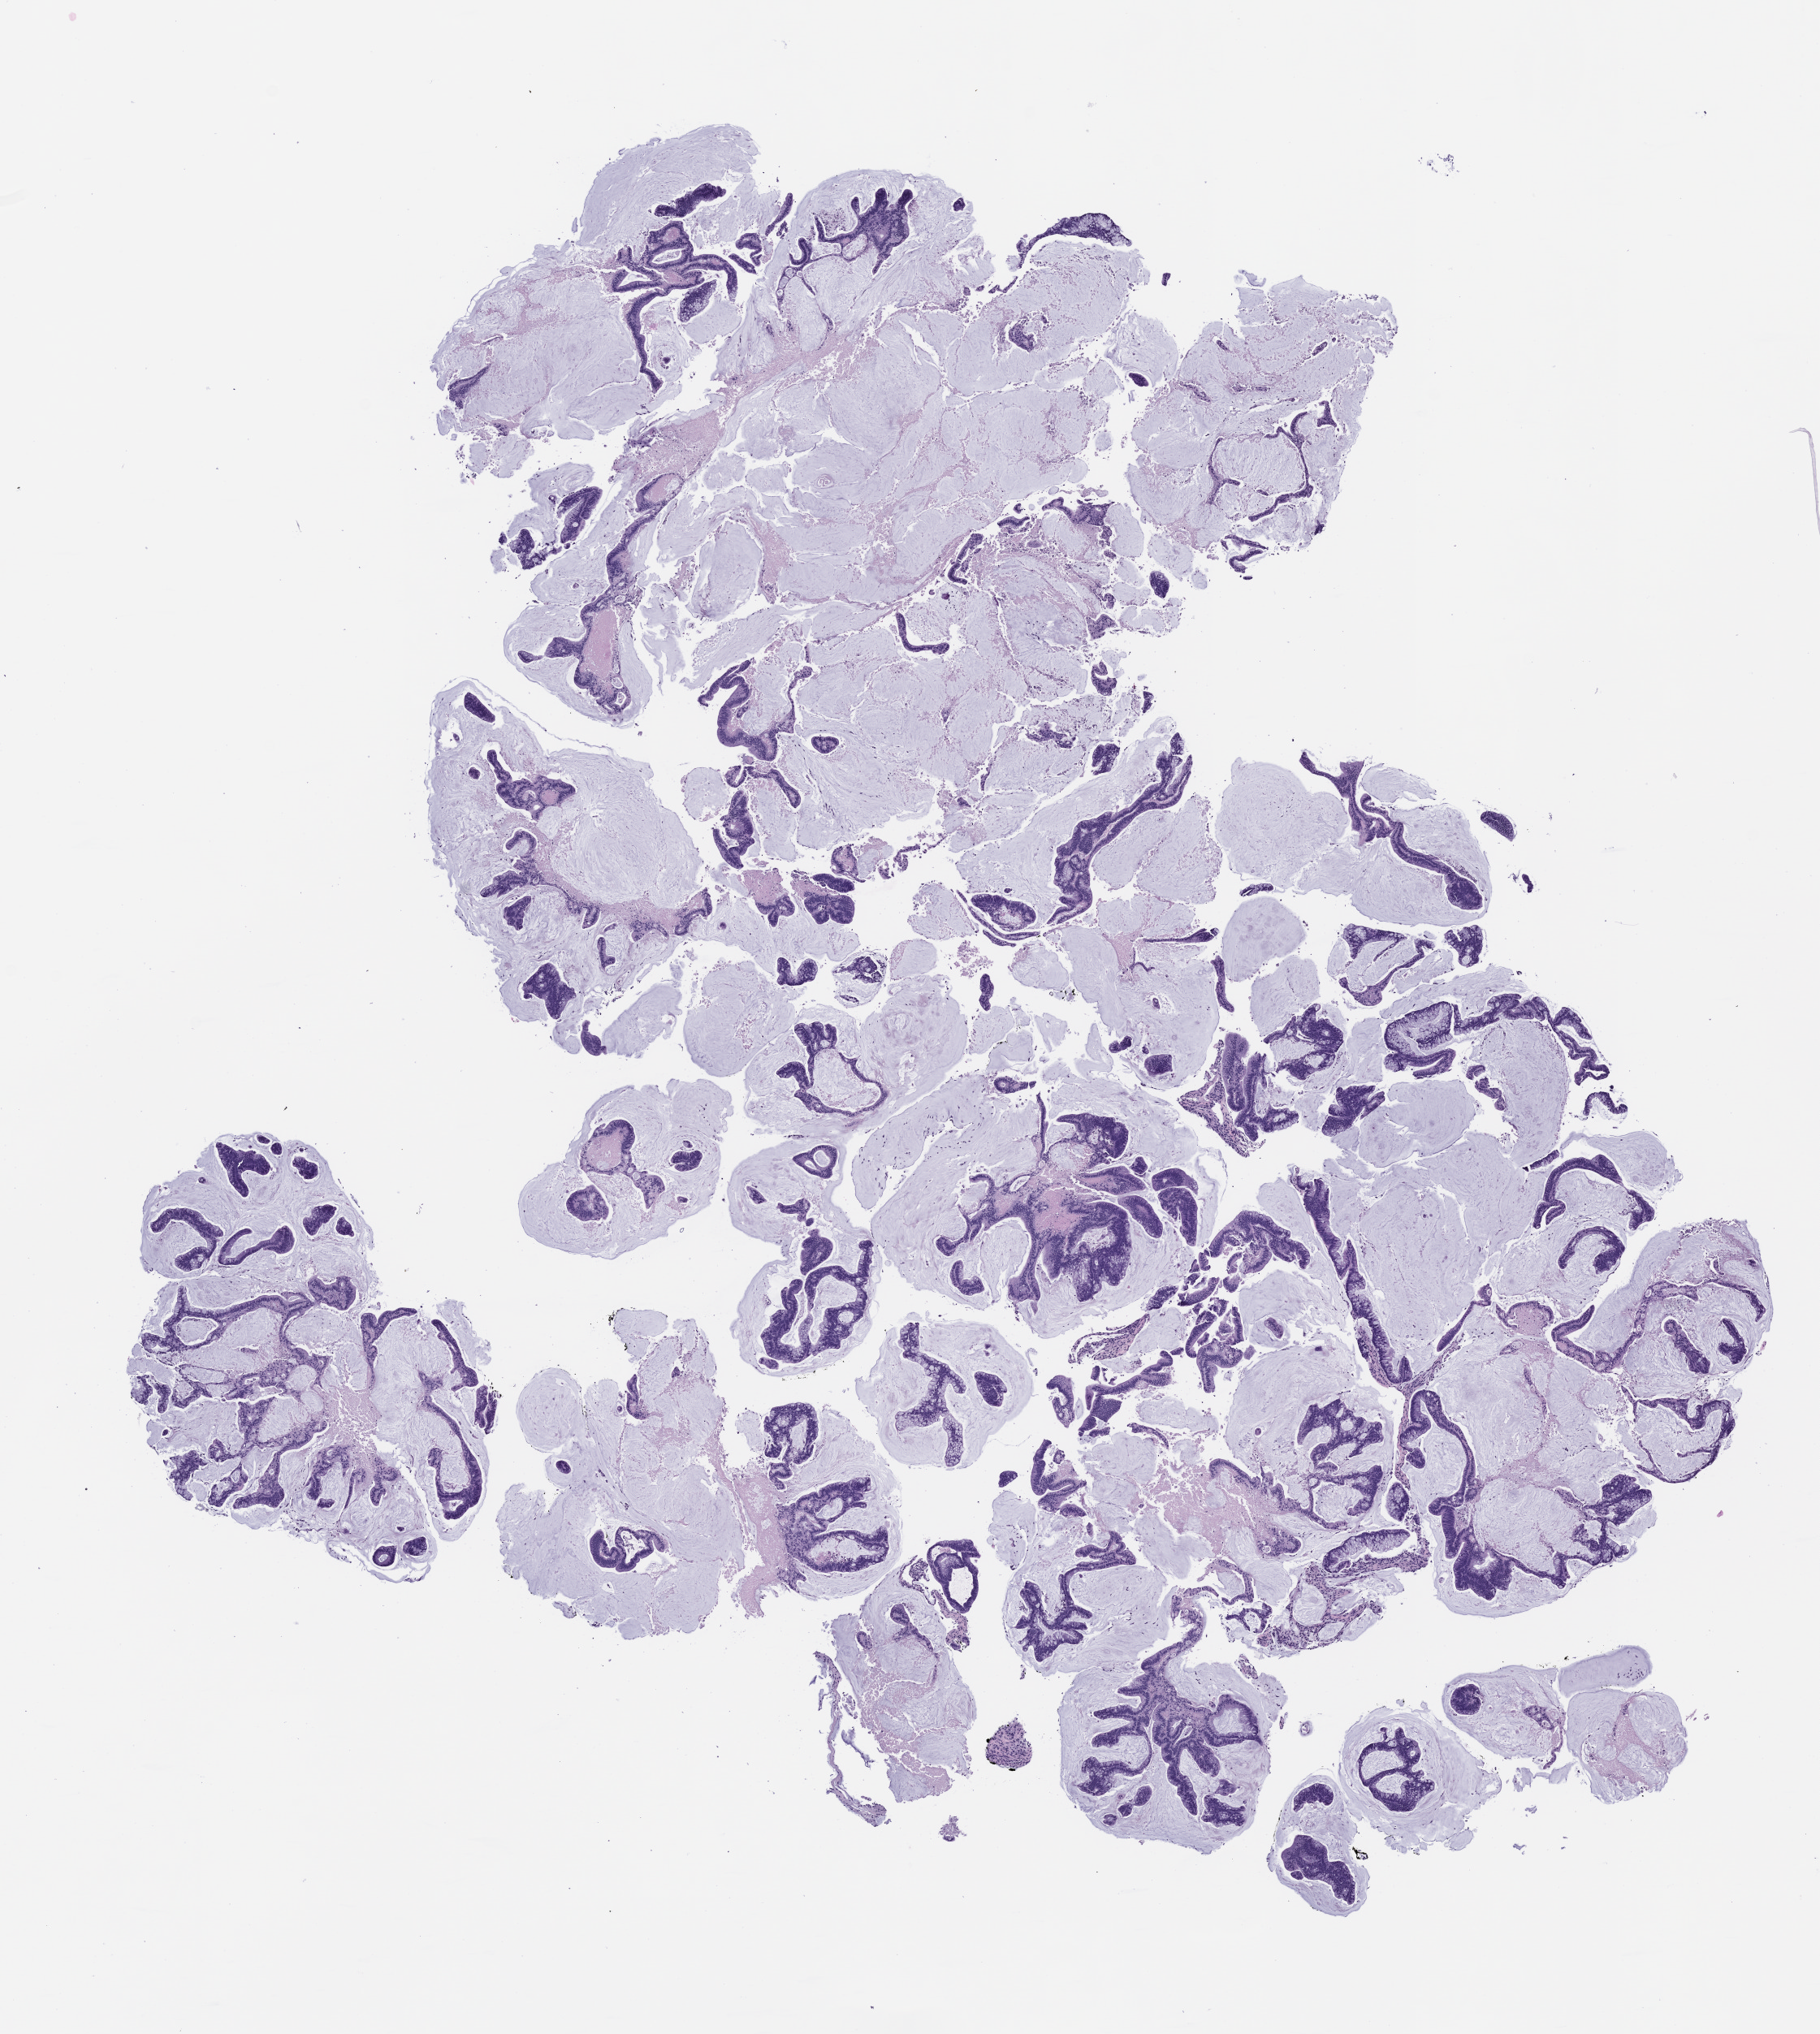
Whole-slide image, H&E: patient-derived xenograft (human tumor grown in a mouse), passage 2 — a low-resolution overview of the entire scanned area, about 9.0 x 10.1 mm. Formalin-fixed, paraffin-embedded (FFPE) tissue. Originating tumor site category: colon.
• originating patient diagnosis: Colon Adenocarcinoma